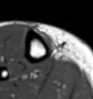
MRI of an extremity soft-tissue mass, one axial slice; position 12 of 54 along the scan axis; MR volume resampled by the dataset authors to the PET/CT grid (not the native acquisition matrix); 3.27 mm slice thickness; 93 × 99 image matrix, field of view 91 × 97 mm. Female patient. Case-level facts recorded for this patient, not image findings: histological type: undifferentiated – high grade; grade: high; site of the primary tumour: right thigh.
Outlined on this slice (expert contour drawn on MRI and transferred to this co-registered scan by the dataset authors):
- gross tumour volume (mass): bounding box [x1, y1, x2, y2] px = [38, 32, 53, 49]